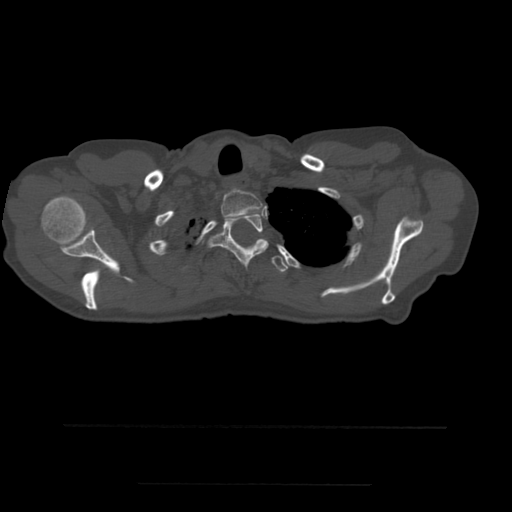
CT including the spine, one axial slice; position 434 of 544 along the scan axis; bone window (W 1800 / L 400 HU); 1.25 mm slice thickness; 512 × 512 image matrix. Patient age 58 years. Case-level facts recorded for this patient, not image findings: primary cancer: lung.
Annotated regions visible in this slice (semi-automatically segmented with operator editing):
- T1 vertebra: bounding box <221,189,263,218> (left, top, right, bottom; pixels)
- T2 vertebra: <205,210,269,266>
- T3 vertebra: <272,255,288,274>